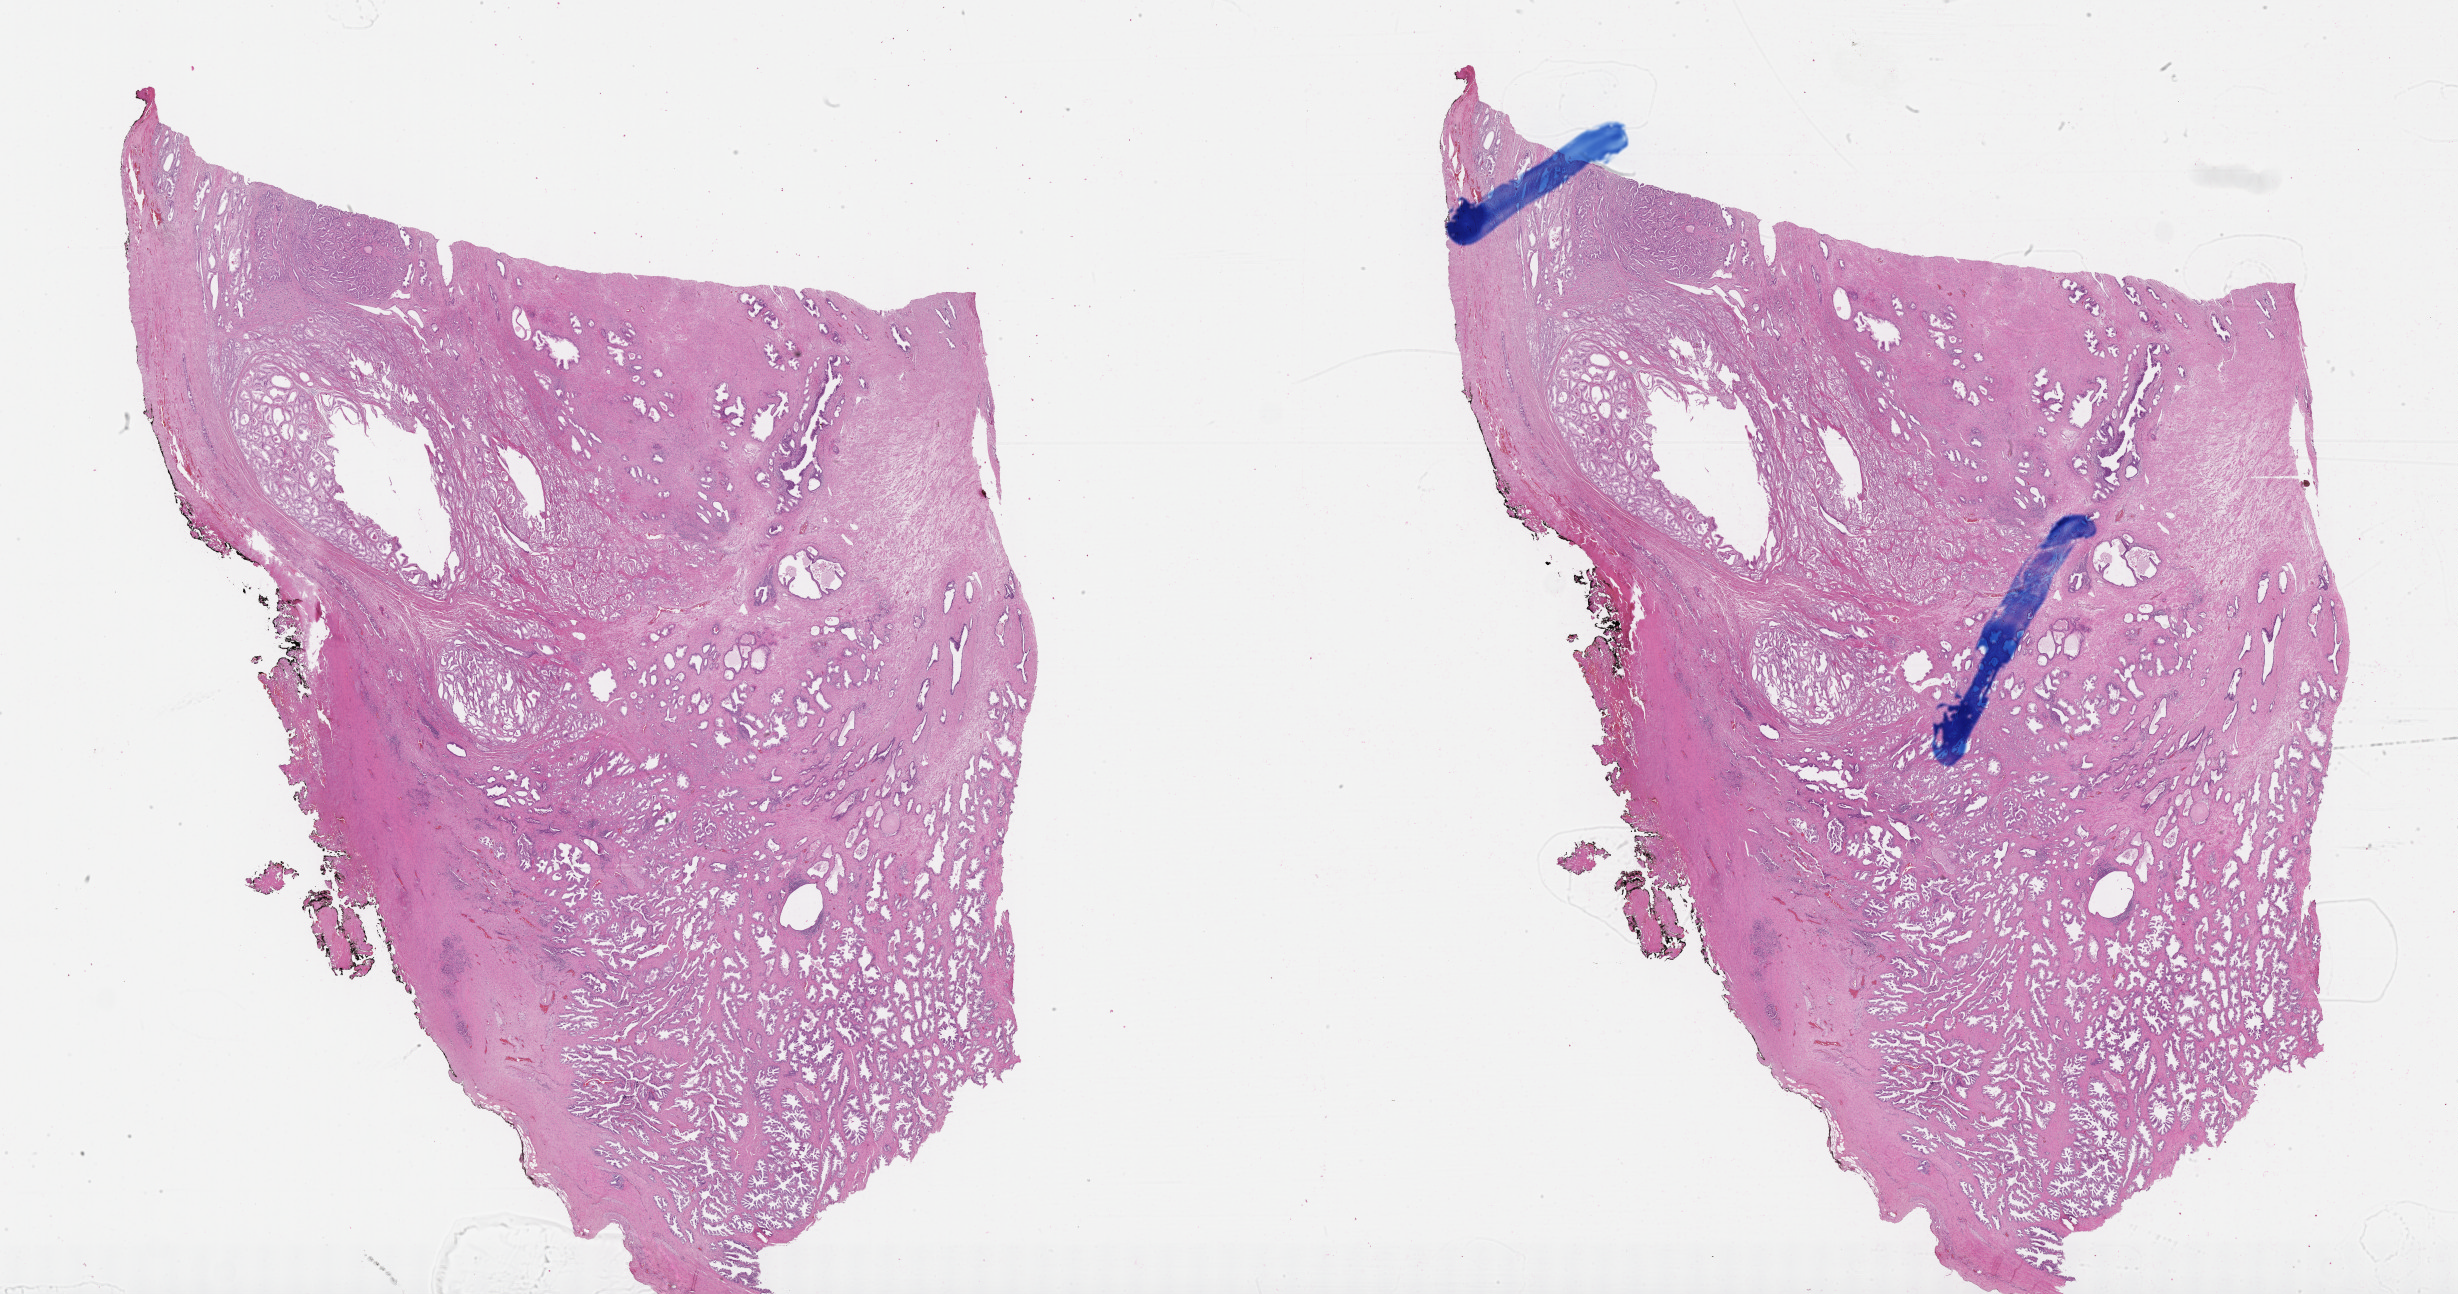
Whole-slide histology image, H&E, low-resolution overview of the scanned area, about 39.8 x 20.9 mm, FFPE section, primary tumour sample from the prostate. Male, age 68 years at initial diagnosis. Gleason score: 7 (3+4).
- laterality: bilateral
- lymph nodes positive (case pathology): 0 of 1 examined
- pathologic diagnosis: Adenocarcinoma, NOS (prostate gland)